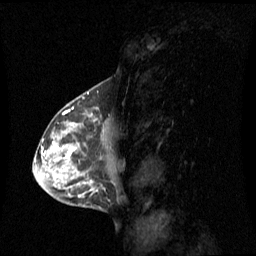
Breast MRI (dynamic contrast-enhanced), one sagittal slice; dynamic contrast-enhanced series, image 2 of 3 at this slice position (ordered by acquisition); 1.5 T; TE 4.2 ms, TR 8.4 ms; 2 mm slice thickness; 256 × 256 image matrix, field of view 270 × 270 mm. Patient: female, 42 years. Case-level facts recorded for this patient, not image findings: setting: breast cancer imaged before/during neoadjuvant chemotherapy; receptor status: HR-positive, HER2-negative.
Outlined on this slice (semi-automatic segmentation, software-assisted and operator-edited):
- analysis volume of interest (the breast-tissue region the enhancement analysis was run in; not a lesion): bounding box (x1, y1, x2, y2) in pixels: (56, 113, 109, 185)
- tumour enhancement mask (voxels above the 70 % enhancement threshold inside the analysis volume of interest): (66, 115, 91, 158)